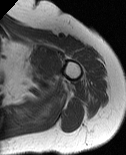
MRI of an extremity soft-tissue mass, one axial slice. Position 66 of 86 along the scan axis. MR volume resampled by the dataset authors to the PET/CT grid (not the native acquisition matrix). 3.27 mm slice thickness. 126 × 155 image matrix. Female patient. From the clinical record (not read from this slice): histological type: pleiomorphic leiomyosarcoma; grade: high; site of the primary tumour: left biceps.
Annotated regions visible in this slice (expert contour drawn on MRI and transferred to this co-registered scan by the dataset authors):
- gross tumour volume including surrounding oedema: bounding box <33,54,53,78> (left, top, right, bottom; pixels)